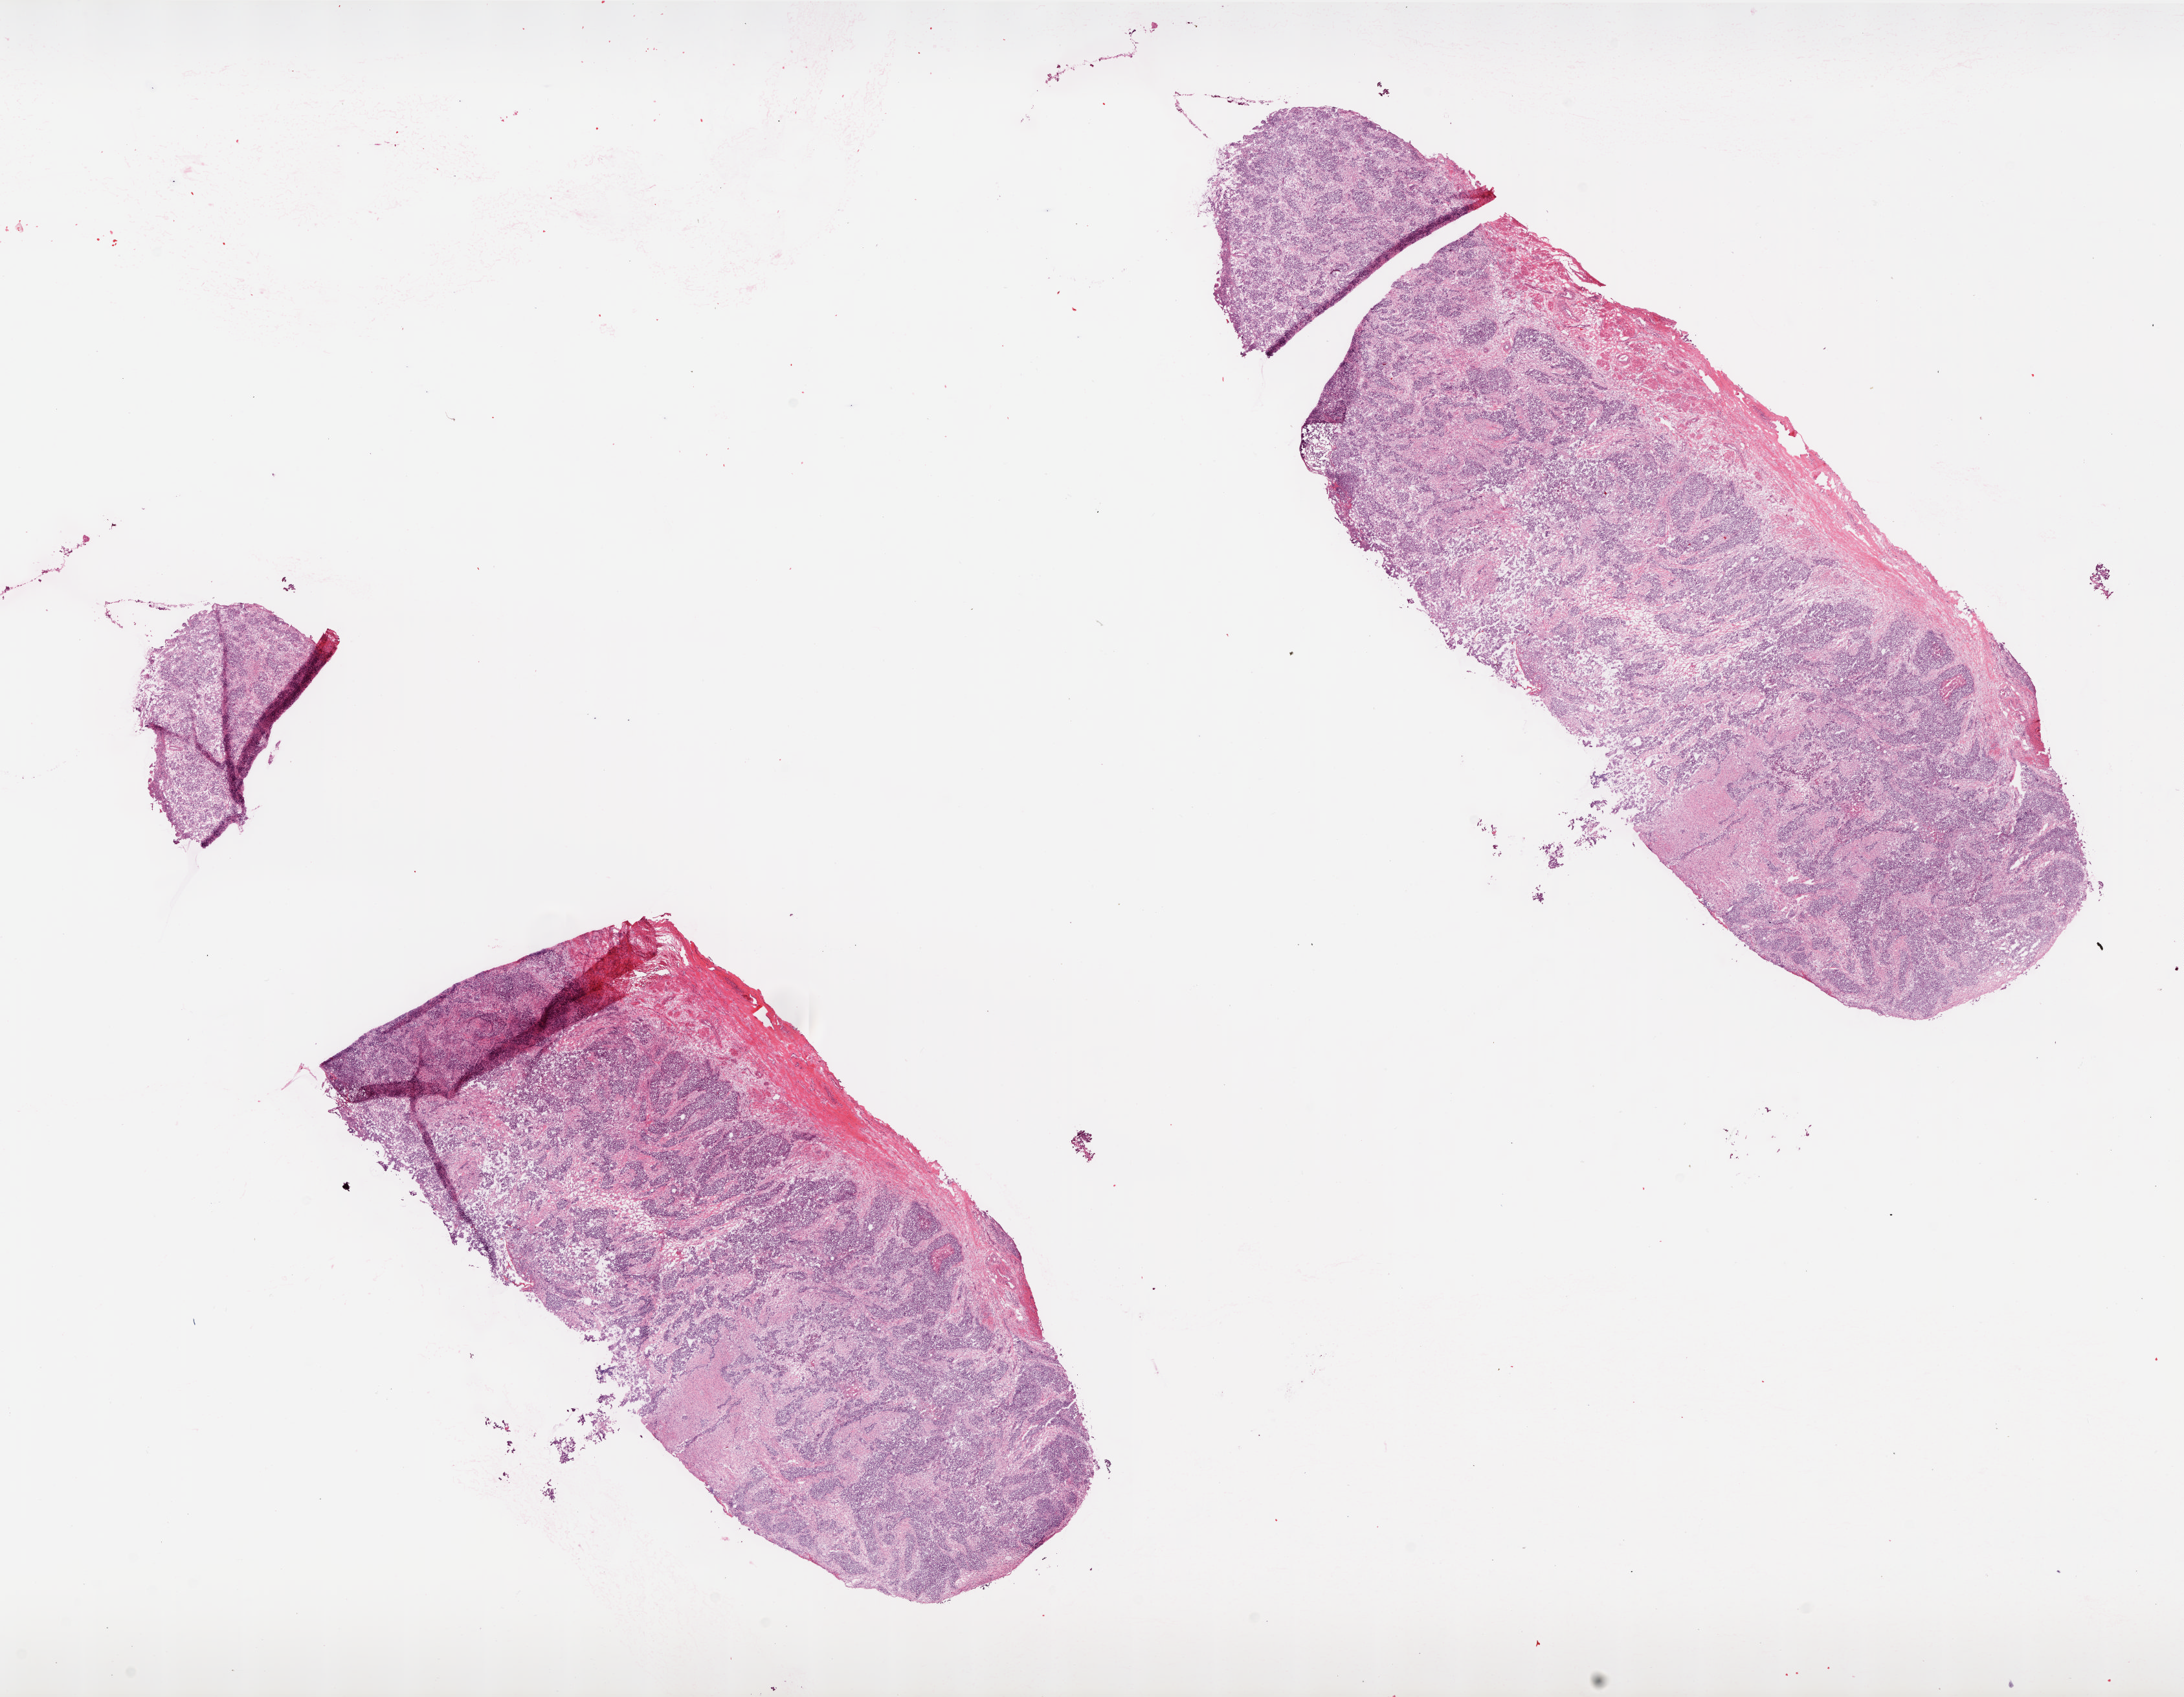
H&E whole-slide image, low-resolution overview of the scanned area, about 26.9 x 20.9 mm. Frozen section from the top of the tissue portion. Sample: primary tumour, ovary. Patient: female, age at initial diagnosis 78 years. Histologic grade: G3 (poorly differentiated). Pathologist review of this section (percent, as recorded): tumour cells 55%, tumour nuclei 85%, stromal cells 30%, necrosis 15%.
- histologic diagnosis: Serous cystadenocarcinoma, NOS
- FIGO stage: IIIC